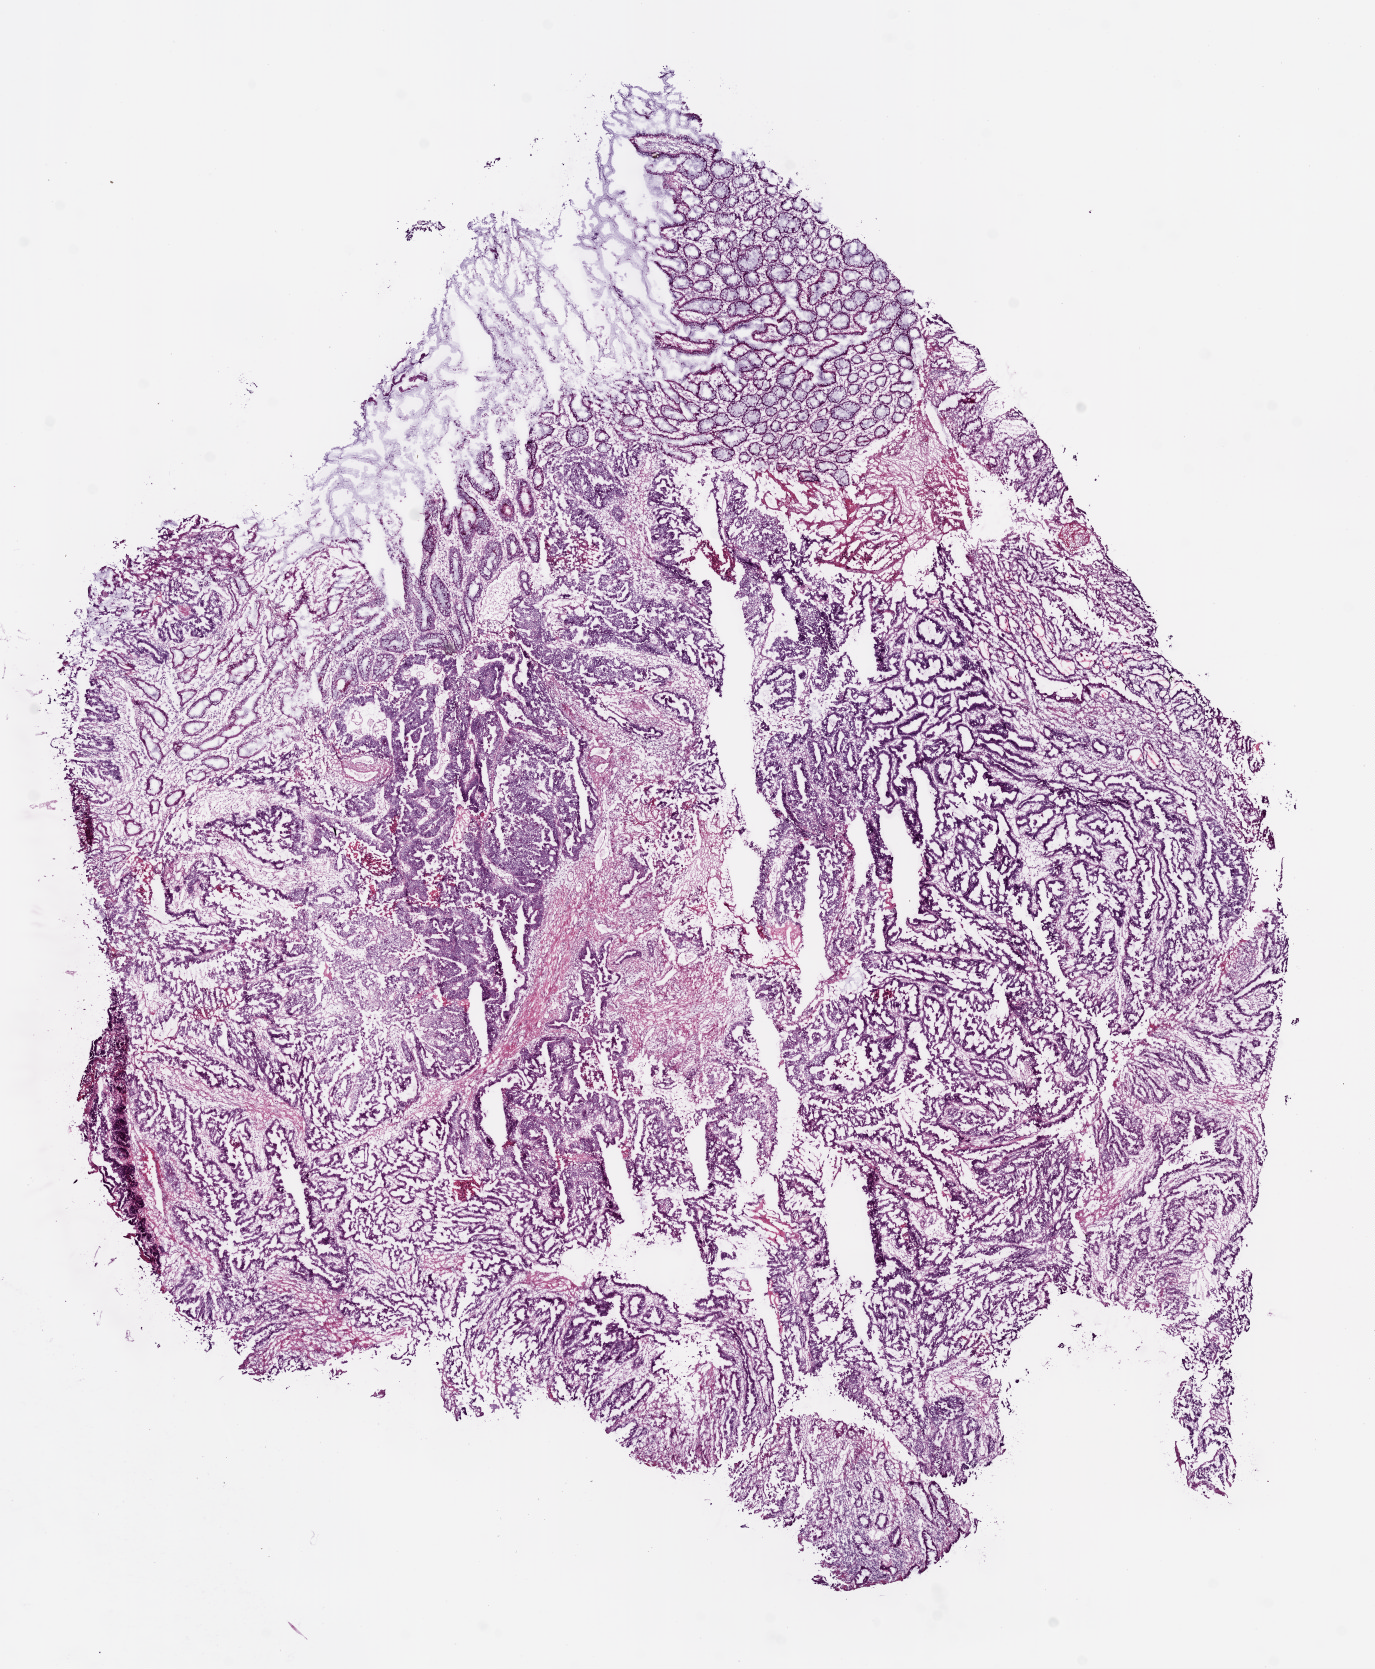
H&E-stained whole-slide image, low-resolution overview of the scanned area, about 11.0 x 13.4 mm, frozen section from the top of the tissue portion, sample: primary tumour, colon. Male patient; age at initial diagnosis 61 years. Composition of this section per pathologist review: tumour cells 72%, tumour nuclei 75%.
Histologic diagnosis: Adenocarcinoma, NOS.